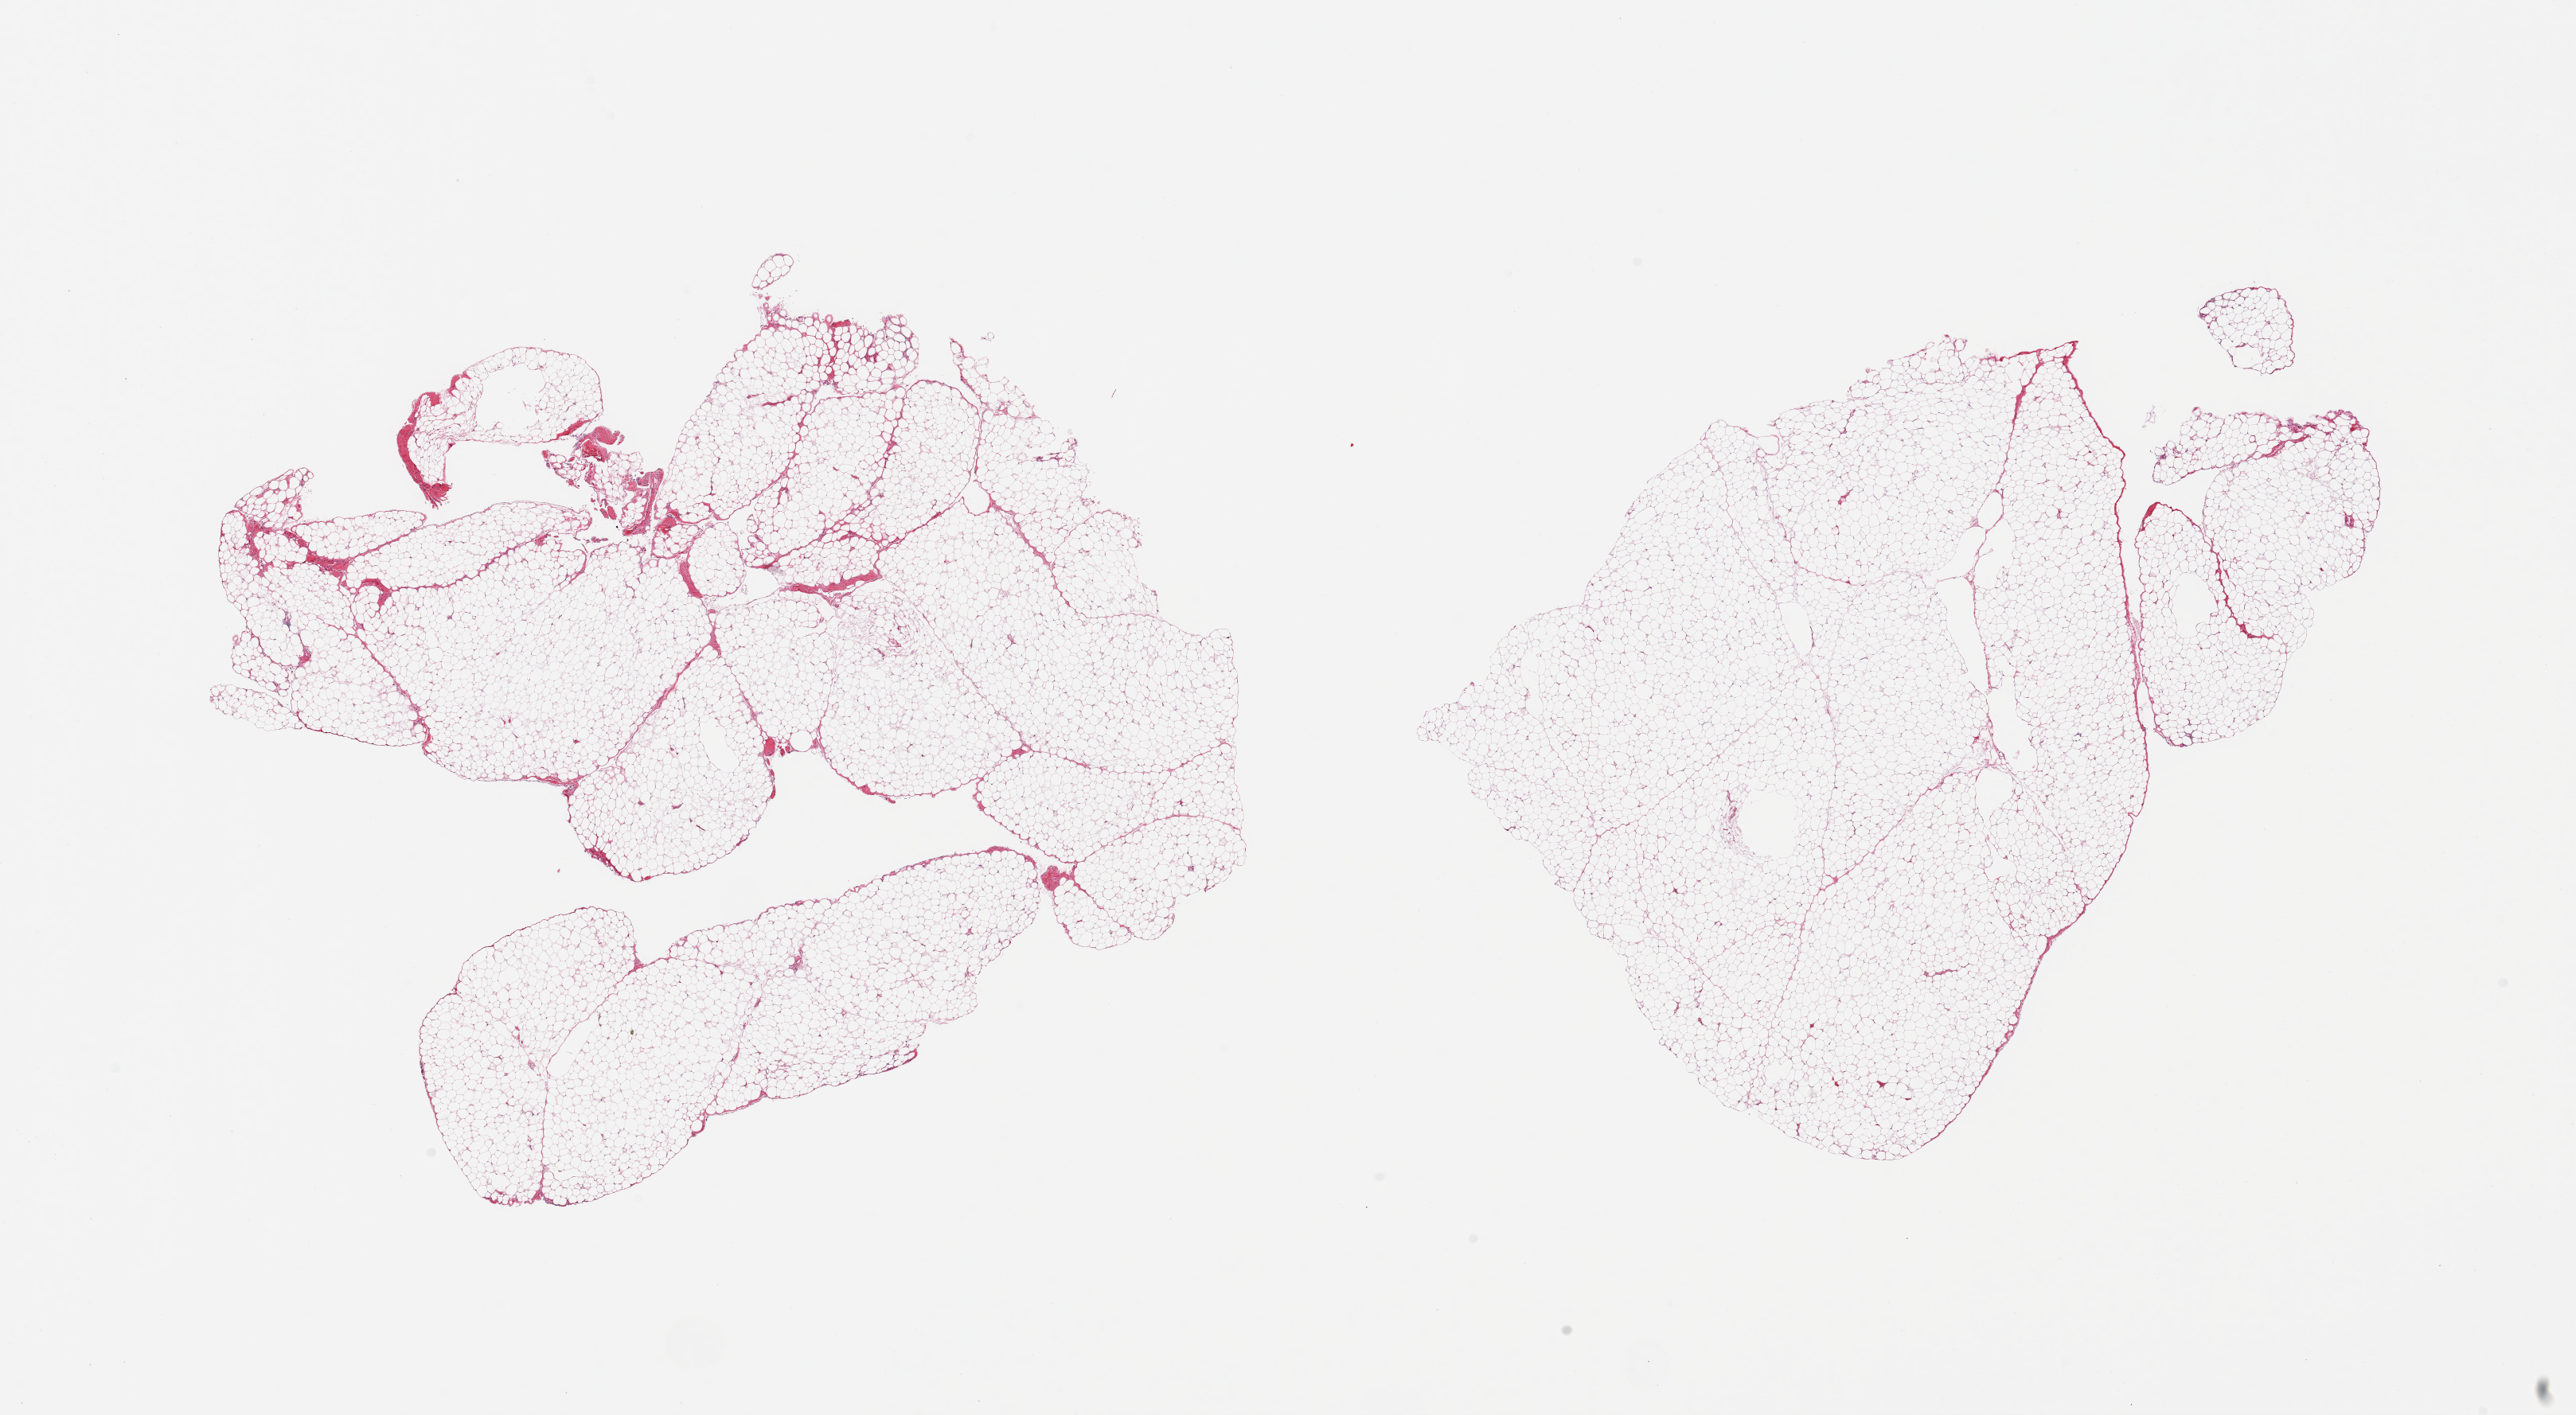
Haematoxylin and eosin whole-slide image — shown as a low-resolution overview of the whole scanned area (about 25.6 x 14.1 mm, from a 20x scan); PAXgene-fixed paraffin-embedded (PFPE) section; section of omentum (target tissue); donor tissue sample. Donor sex: male.
- review note (as recorded): 2 pieces, <5% fascia